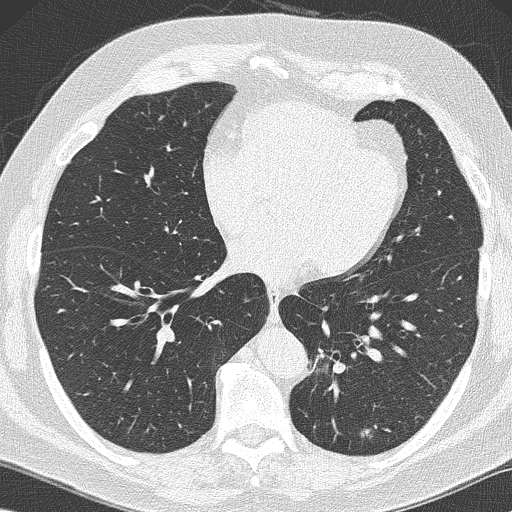
Axial slice from a low-dose chest CT screening exam. Baseline annual screen. Lung window (W 1500 / L -600 HU). 120 kVp. Slice 98 of 152 in the series. 512 × 512 image matrix. Male, age 59 years at enrolment. Former smoker at enrolment.
Expert-annotated lung lesion, bounding box (x1, y1, x2, y2) in pixels: (346, 413, 391, 453). The screening reader recorded 2 non-calcified nodules or masses ≥4 mm on this exam (left lower lobe, left lower lobe); which of them this box marks is not recorded. Official screen result: positive, change unspecified: nodule(s) >= 4 mm or enlarging nodule(s), mass(es), or other non-specific abnormalities suspicious for lung cancer.